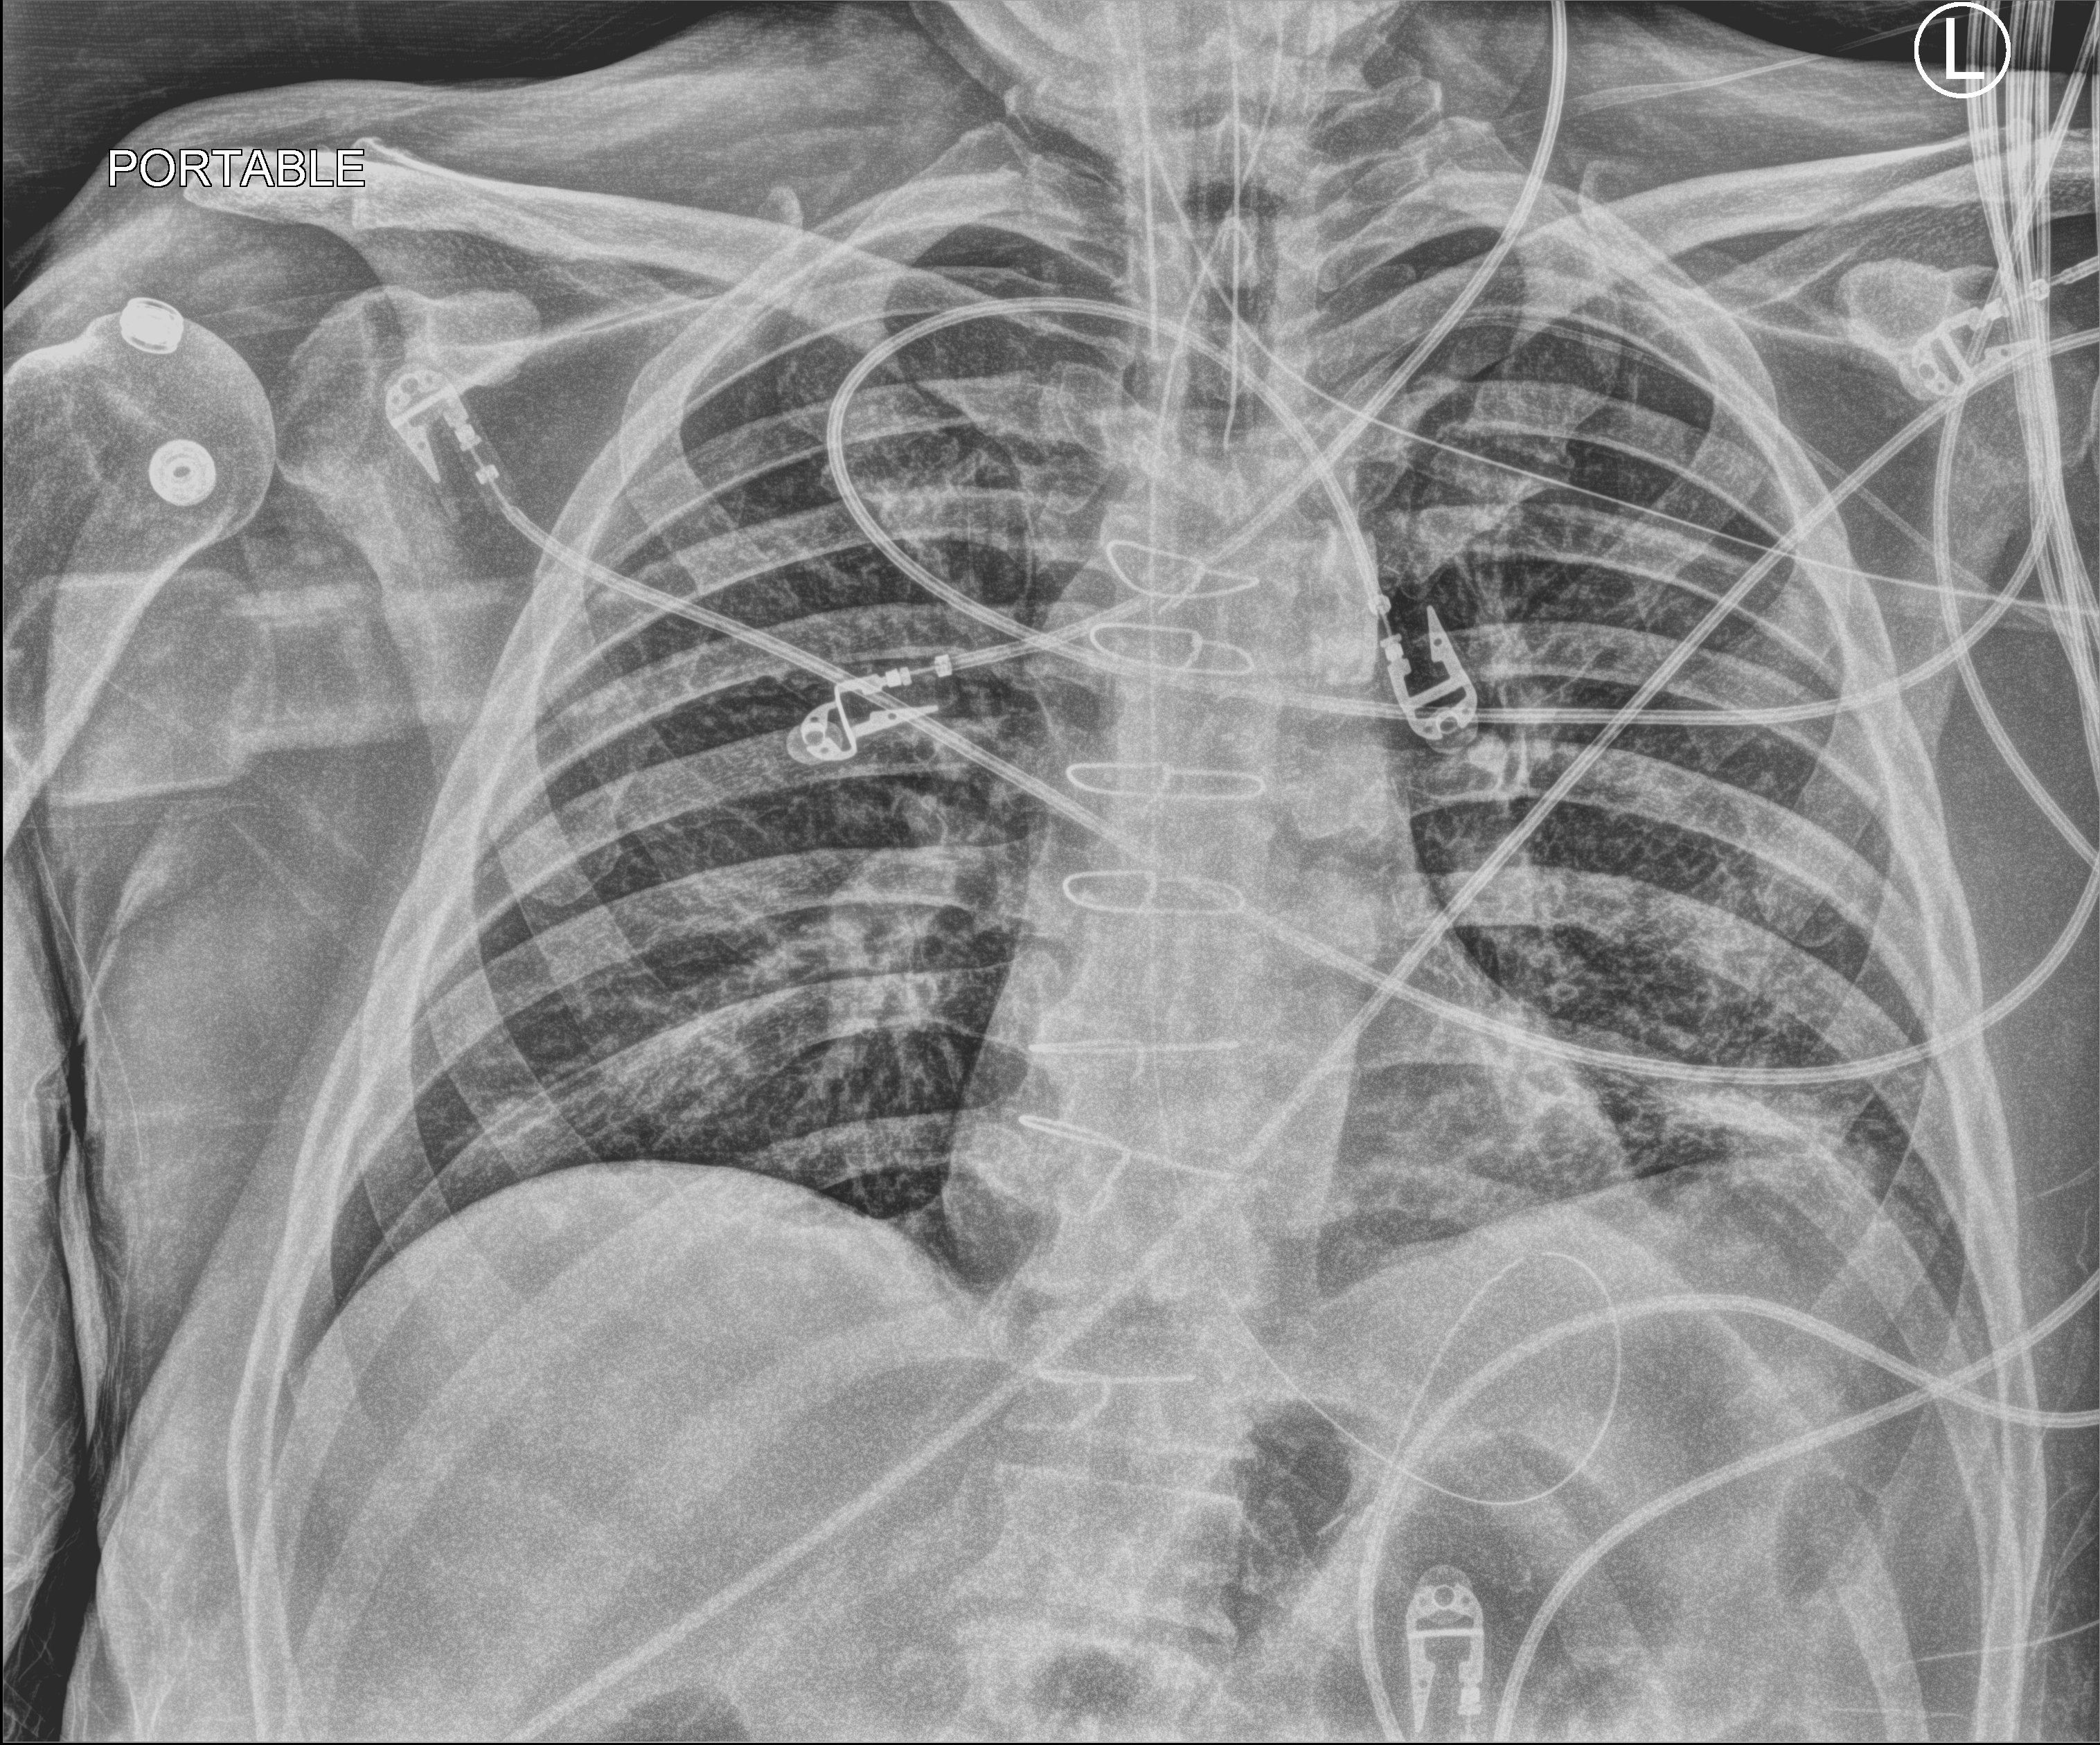
Portable chest radiograph; anteroposterior (AP) projection. Patient hospitalised with COVID-19; male, aged 60–74 years.
Hospital-stay facts (about this admission, not read from this image; timing relative to this image not recorded): admitted to intensive care during this hospital stay: yes; mechanically ventilated during this hospital stay: yes; COPD (admission record): no.